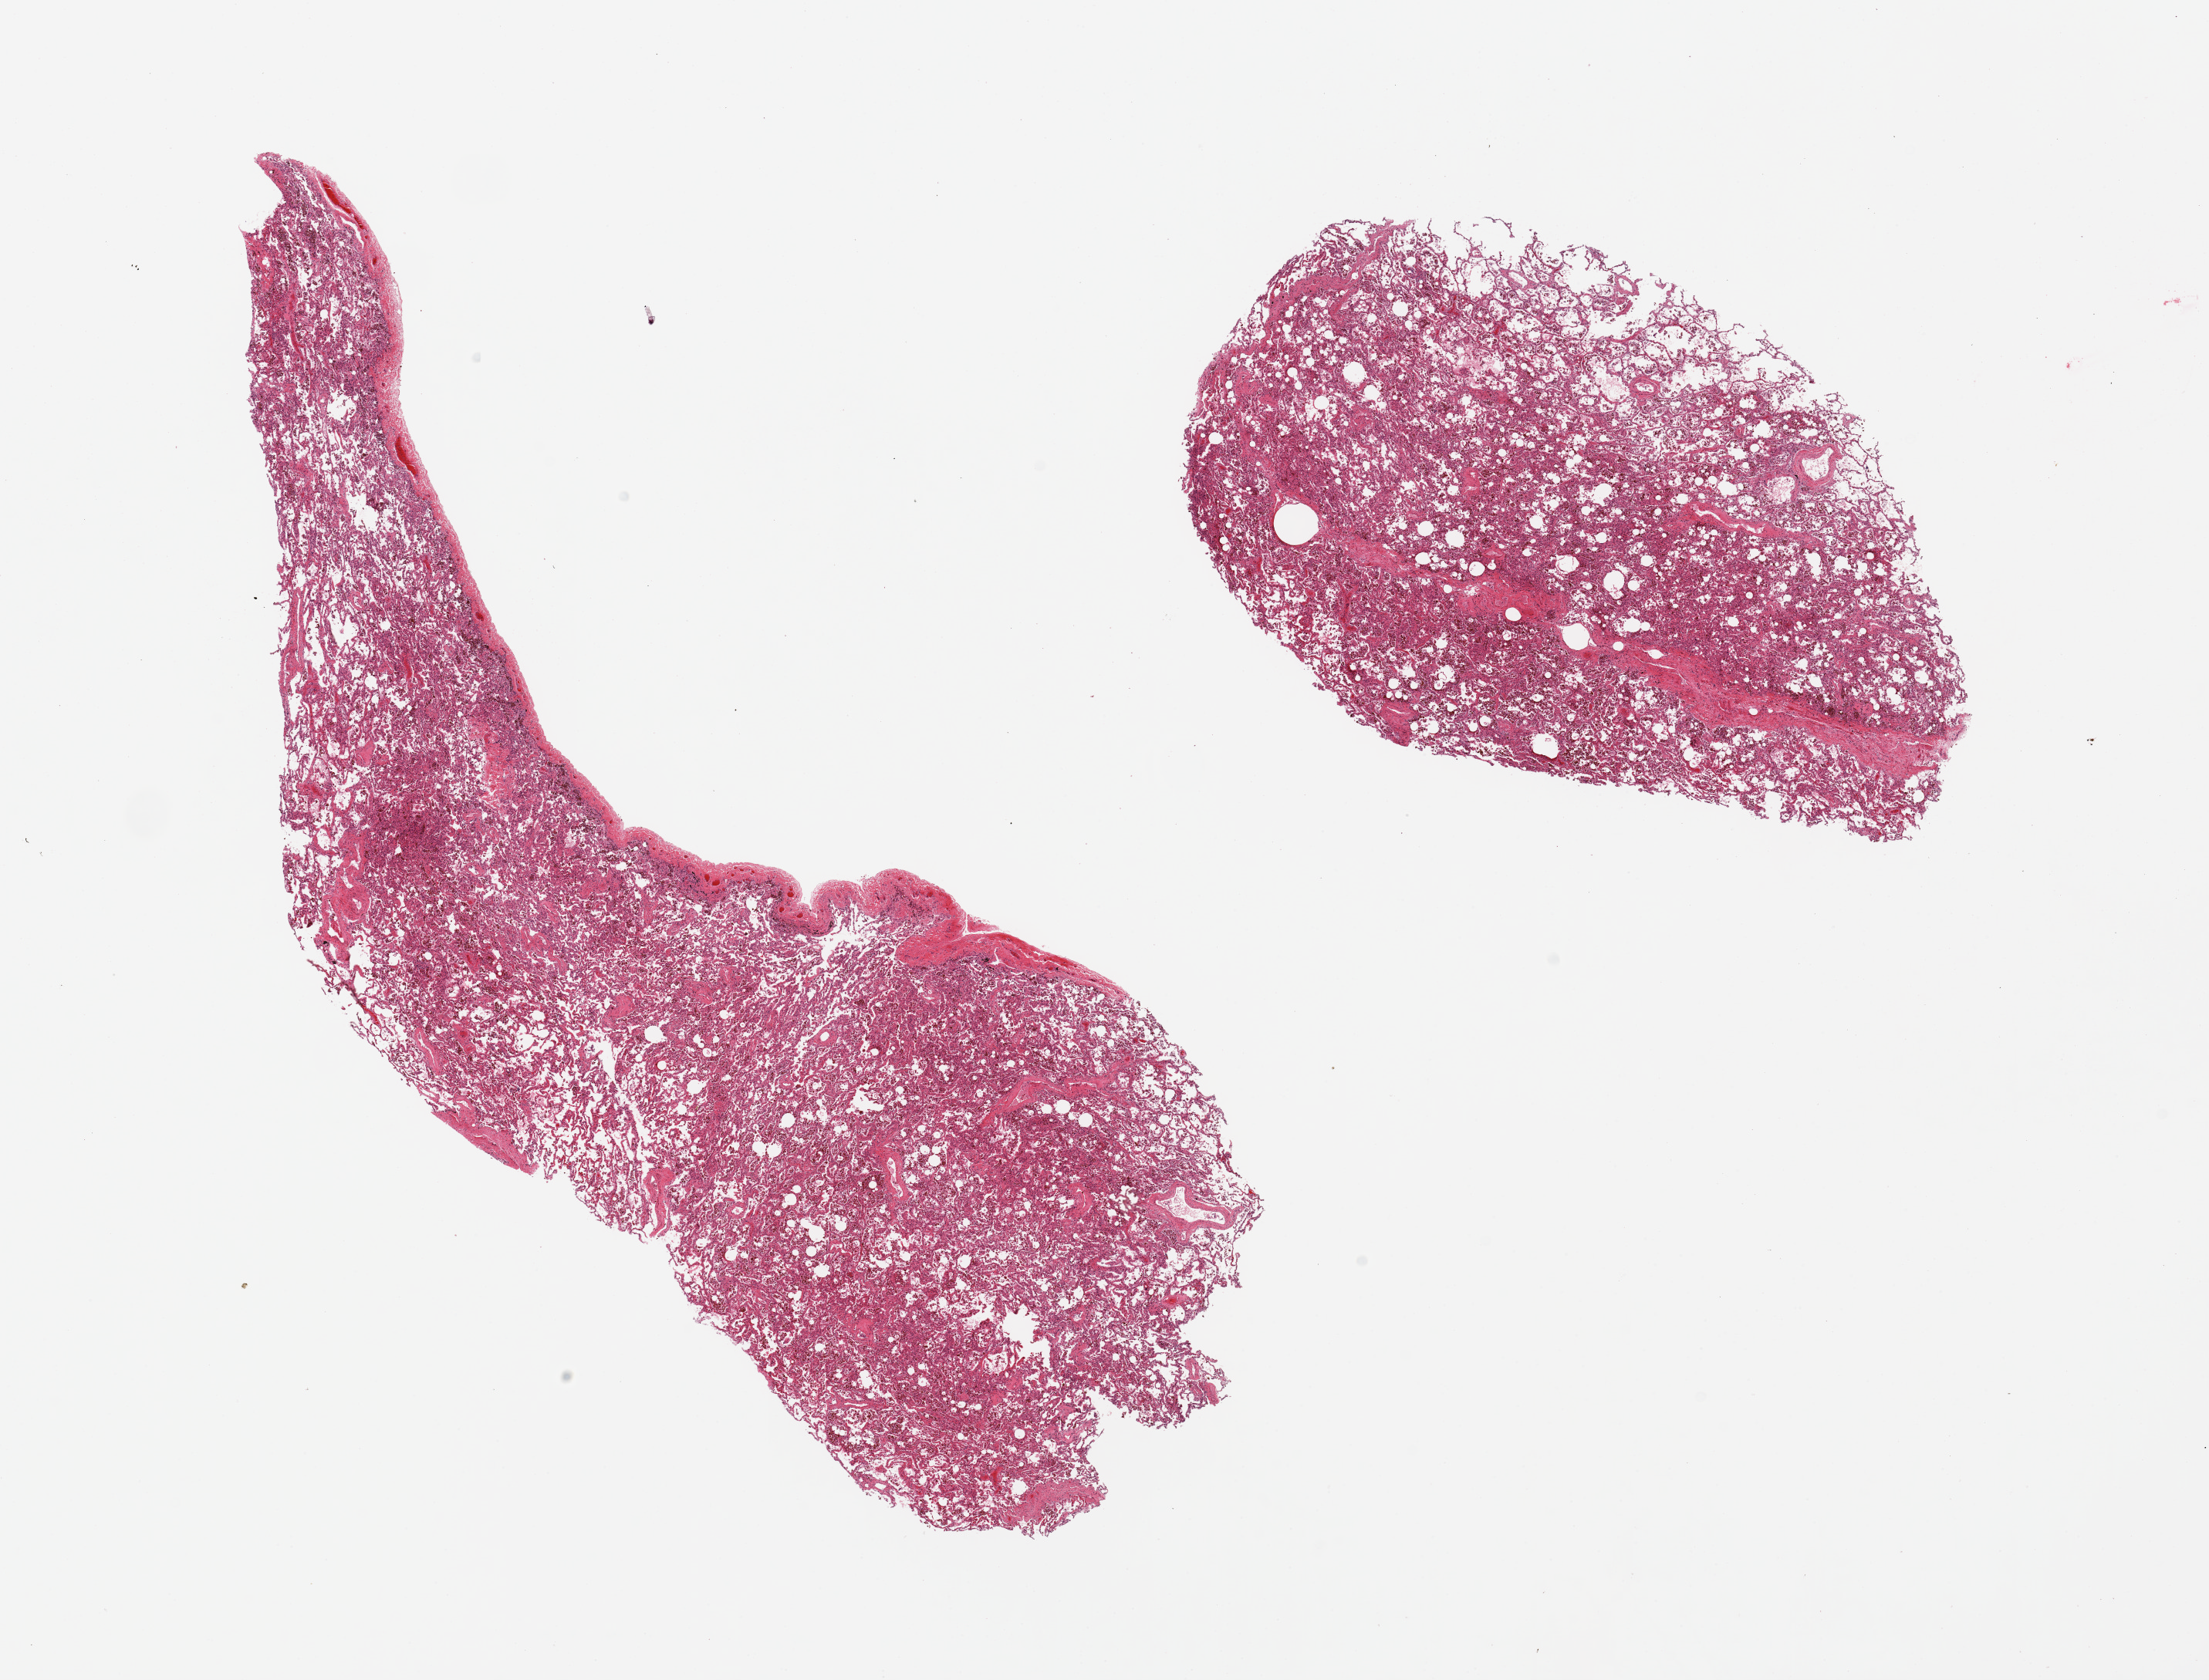
Whole-slide image, hematoxylin and eosin (H&E) stain — a low-resolution overview of the entire scanned area, about 22.6 x 17.2 mm; PAXgene-fixed paraffin-embedded (PFPE) section; target tissue: lung; tissue donor sample.
Reviewer comment on this tissue sample: 2 pieces; pleura present (target is 1cm below pleura), numerous hemosiderin-laden macrophages, some fibrosis.